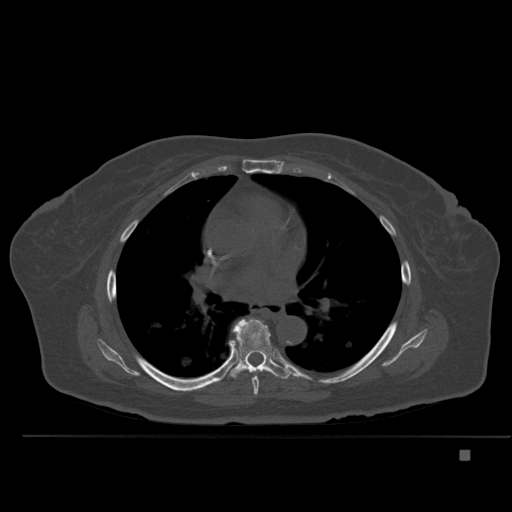
CT including the spine, one axial slice. Slice 330 of 477 in the series (ordered by position). Bone window (W 1800 / L 400 HU). 512 × 512 image matrix. Patient: female, 74 years. Case-level facts recorded for this patient, not image findings: primary cancer: colon.
Structures marked on this image (semi-automatic segmentation, software-assisted and operator-edited):
- T6 vertebra: box from (x=252, y=370) to (x=266, y=396) px
- T7 vertebra: (x=229, y=319)–(x=293, y=379)